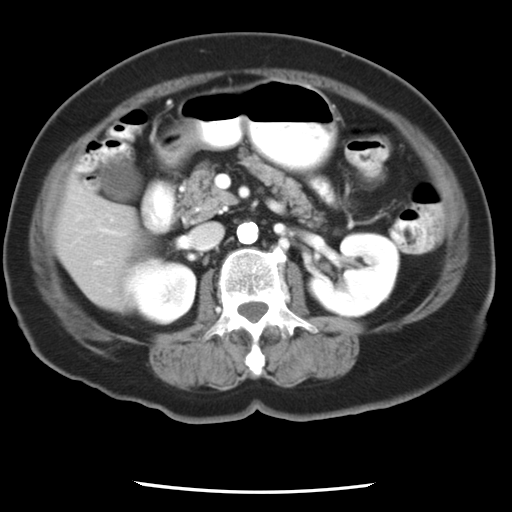
Contrast-enhanced abdominal CT, one axial slice; position 8 of 24 along the scan axis; reconstruction kernel STANDARD; 120 kVp; intravenous contrast given; soft-tissue window (W 400 / L 40 HU); 7.5 mm slice thickness; 512 × 512 image matrix. Female patient, age 71 years. Case-level facts recorded for this patient, not image findings: diagnosis: colorectal cancer liver metastases, imaged before liver resection; multiple liver metastases: no; largest metastasis: 4.3 cm; disease in both lobes: no.
Outlined on this slice (manually delineated by an expert):
- liver: bounding box (x1, y1, x2, y2) in pixels: (56, 179, 147, 309)
- planned liver remnant (the part of the liver to remain after resection): (56, 178, 147, 309)